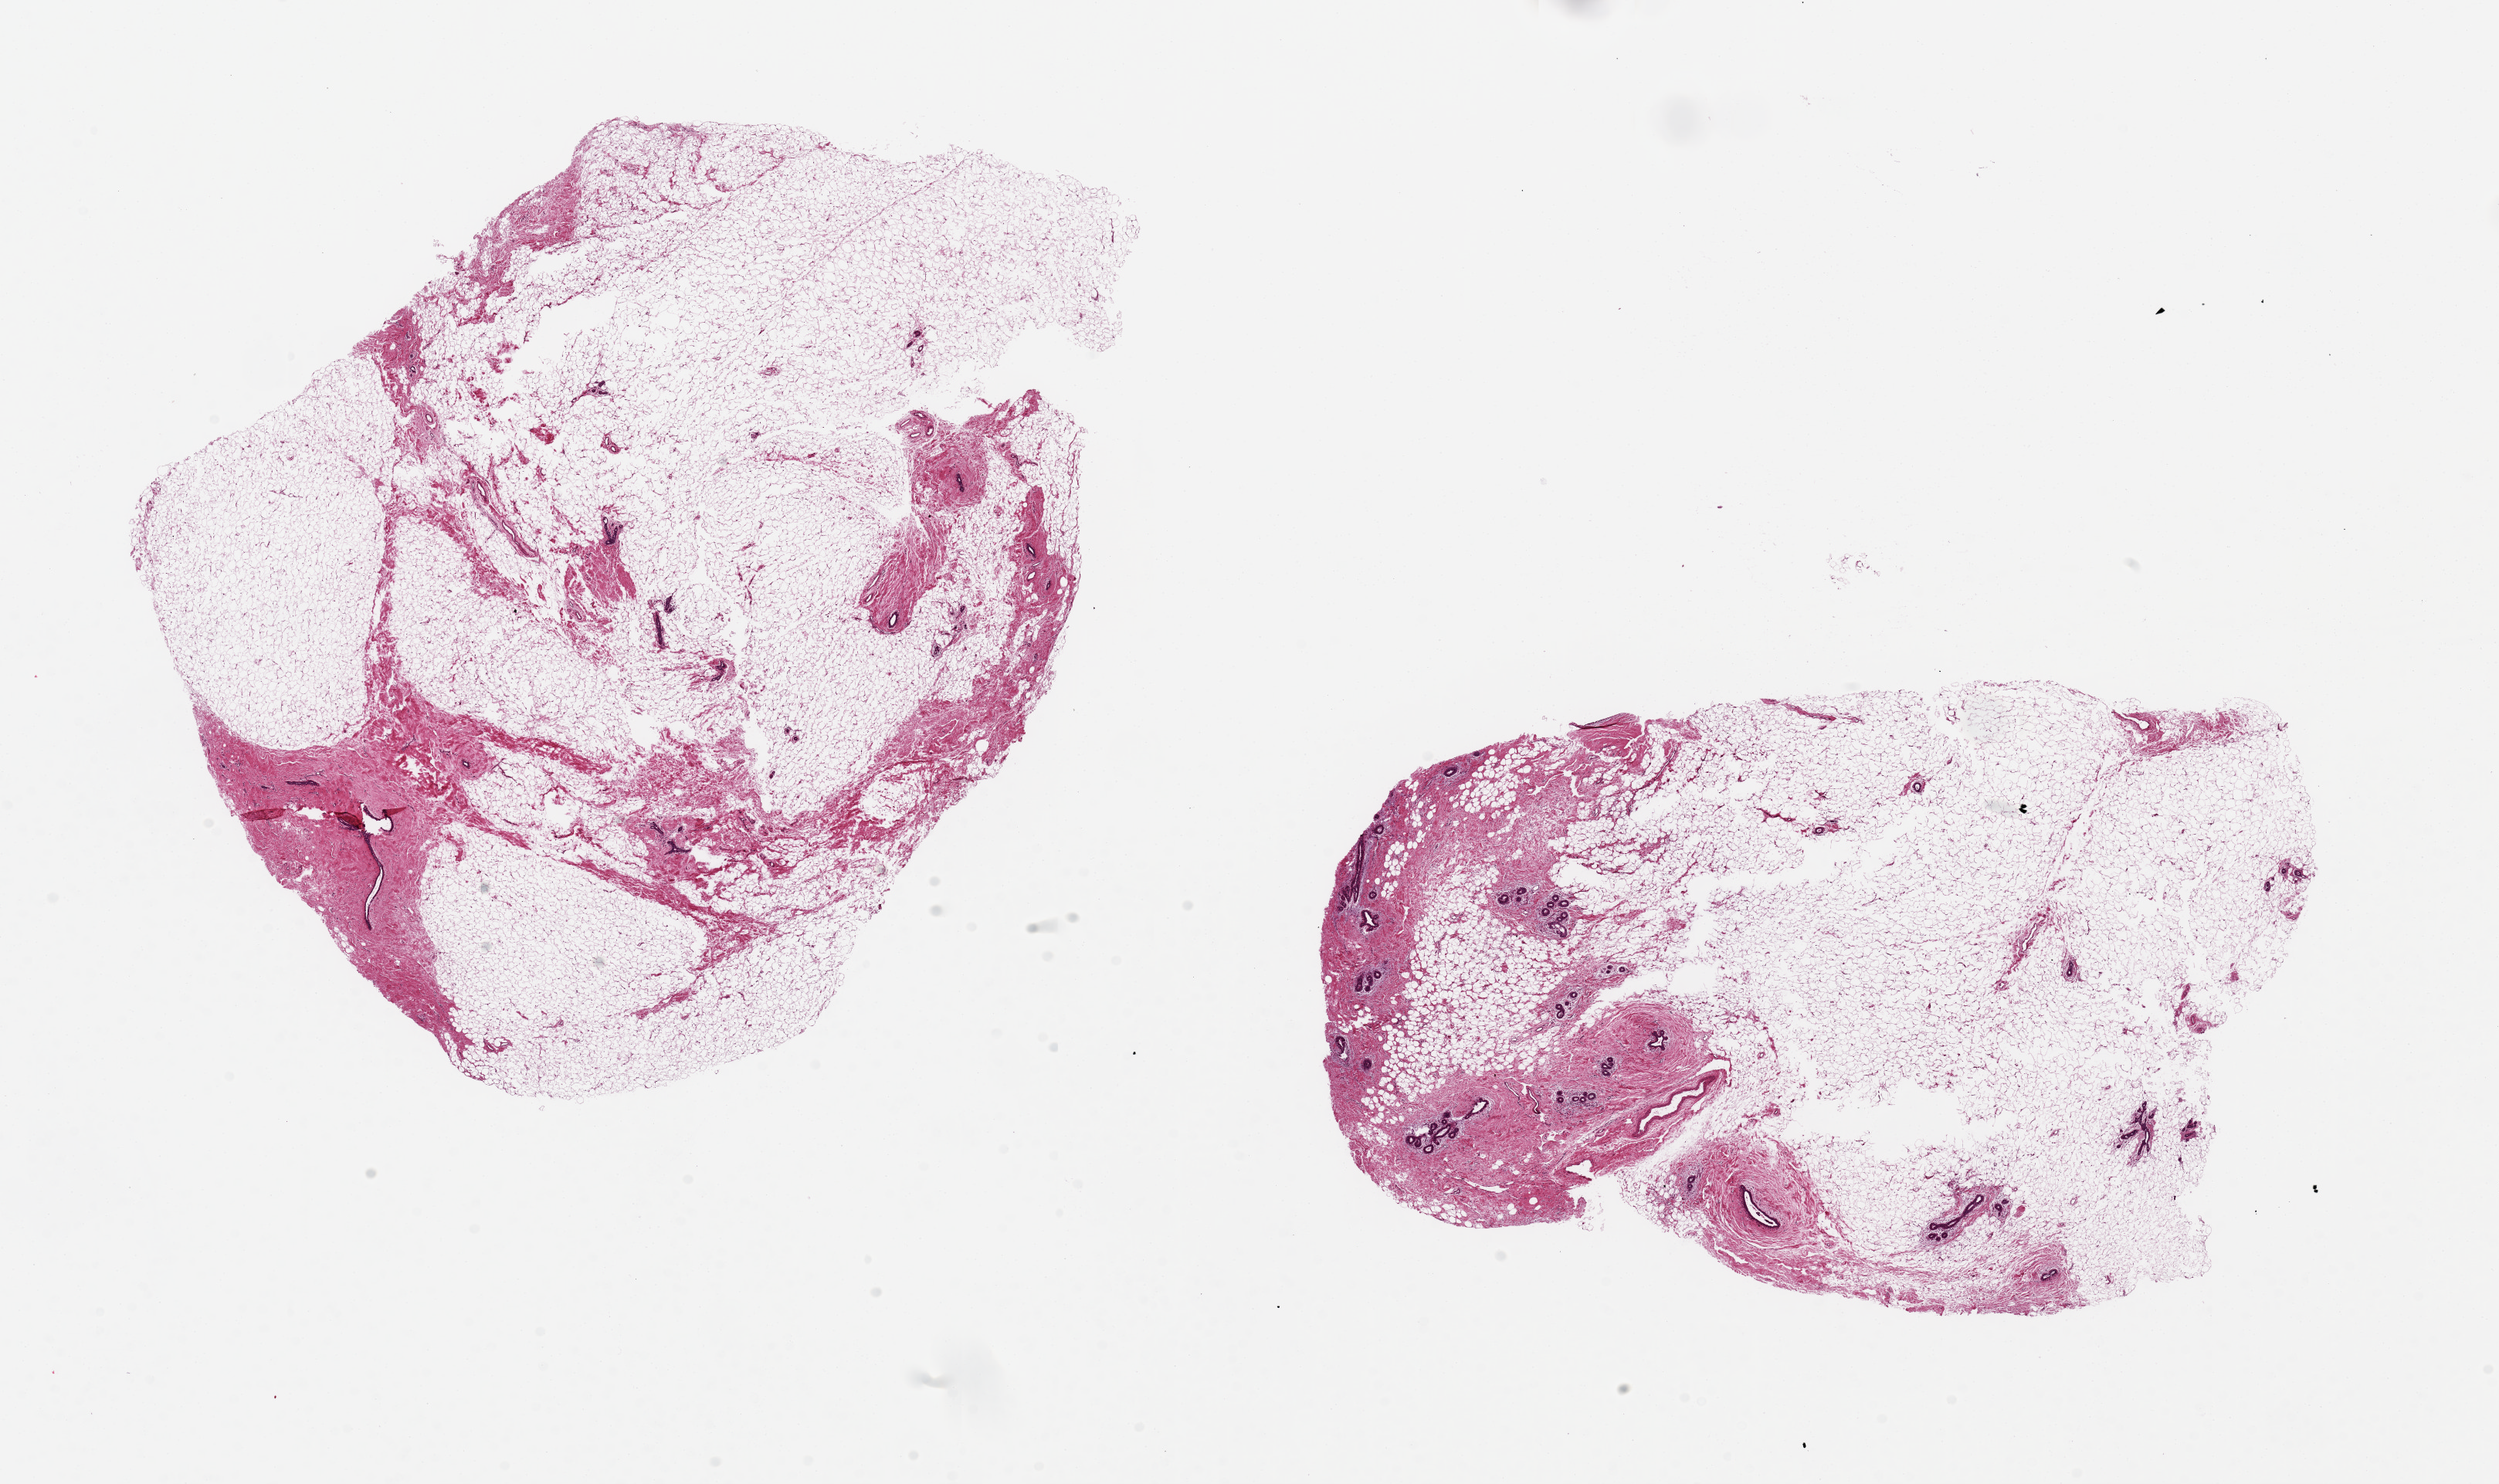
Whole-slide image, hematoxylin and eosin (H&E) stain, brightfield — low-resolution overview of the scanned area, about 25.6 x 15.2 mm, PAXgene-fixed paraffin-embedded (PFPE) section, target tissue: breast, tissue donor sample. Female donor.
• review note (as recorded): 2 pieces 10x7mm, representative TDLUs